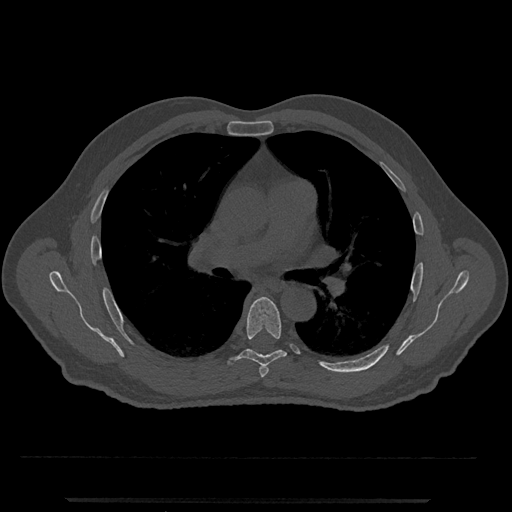
CT including the spine, one axial slice; slice 738 of 797 in the series (ordered by position); 120 kVp; bone window (W 1800 / L 400 HU); 512 × 512 image matrix, field of view 419 × 419 mm. Male patient, age 63 years. Case-level facts recorded for this patient, not image findings: primary cancer: prostate.
Annotated regions visible in this slice (semi-automatic segmentation, software-assisted and operator-edited):
- T5 vertebra: bounding box <259,364,269,378> (left, top, right, bottom; pixels)
- T6 vertebra: <228,297,287,367>